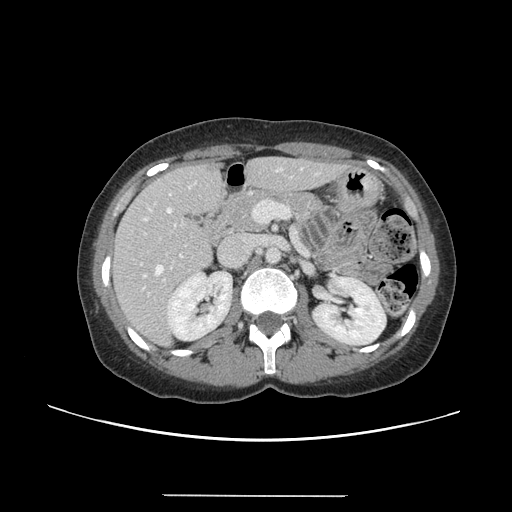
Contrast-enhanced abdominal CT, one axial slice; position 71 of 144 along the scan axis; intravenous contrast given; soft-tissue window (W 400 / L 40 HU); 2.5 mm slice thickness; 512 × 512 image matrix, field of view 380 × 380 mm. Female patient, age 53 years. Case-level facts recorded for this patient, not image findings: diagnosis: colorectal cancer liver metastases, imaged before liver resection; multiple liver metastases: yes; largest metastasis: 1.1 cm; disease in both lobes: no.
Annotated regions visible in this slice (manually delineated by an expert):
- hepatic veins: box from (x=143, y=168) to (x=282, y=277) px
- liver: (x=113, y=159)–(x=340, y=344)
- planned liver remnant (the part of the liver to remain after resection): (x=113, y=159)–(x=322, y=302)
- portal vein (with intrahepatic branches): (x=141, y=200)–(x=290, y=296)